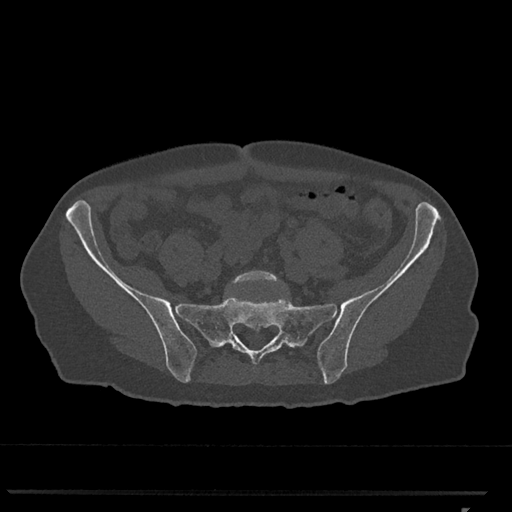
CT including the spine, one axial slice; slice 107 of 793 in the series (ordered by position); reconstruction kernel Br40s/3; bone window (W 1800 / L 400 HU); 512 × 512 image matrix, field of view 380 × 380 mm. Female patient, age 62 years. From the clinical record (not read from this slice): primary cancer: renal.
Annotated regions visible in this slice (semi-automatic segmentation, software-assisted and operator-edited):
- L5 vertebra: box from (x=231, y=271) to (x=281, y=286) px